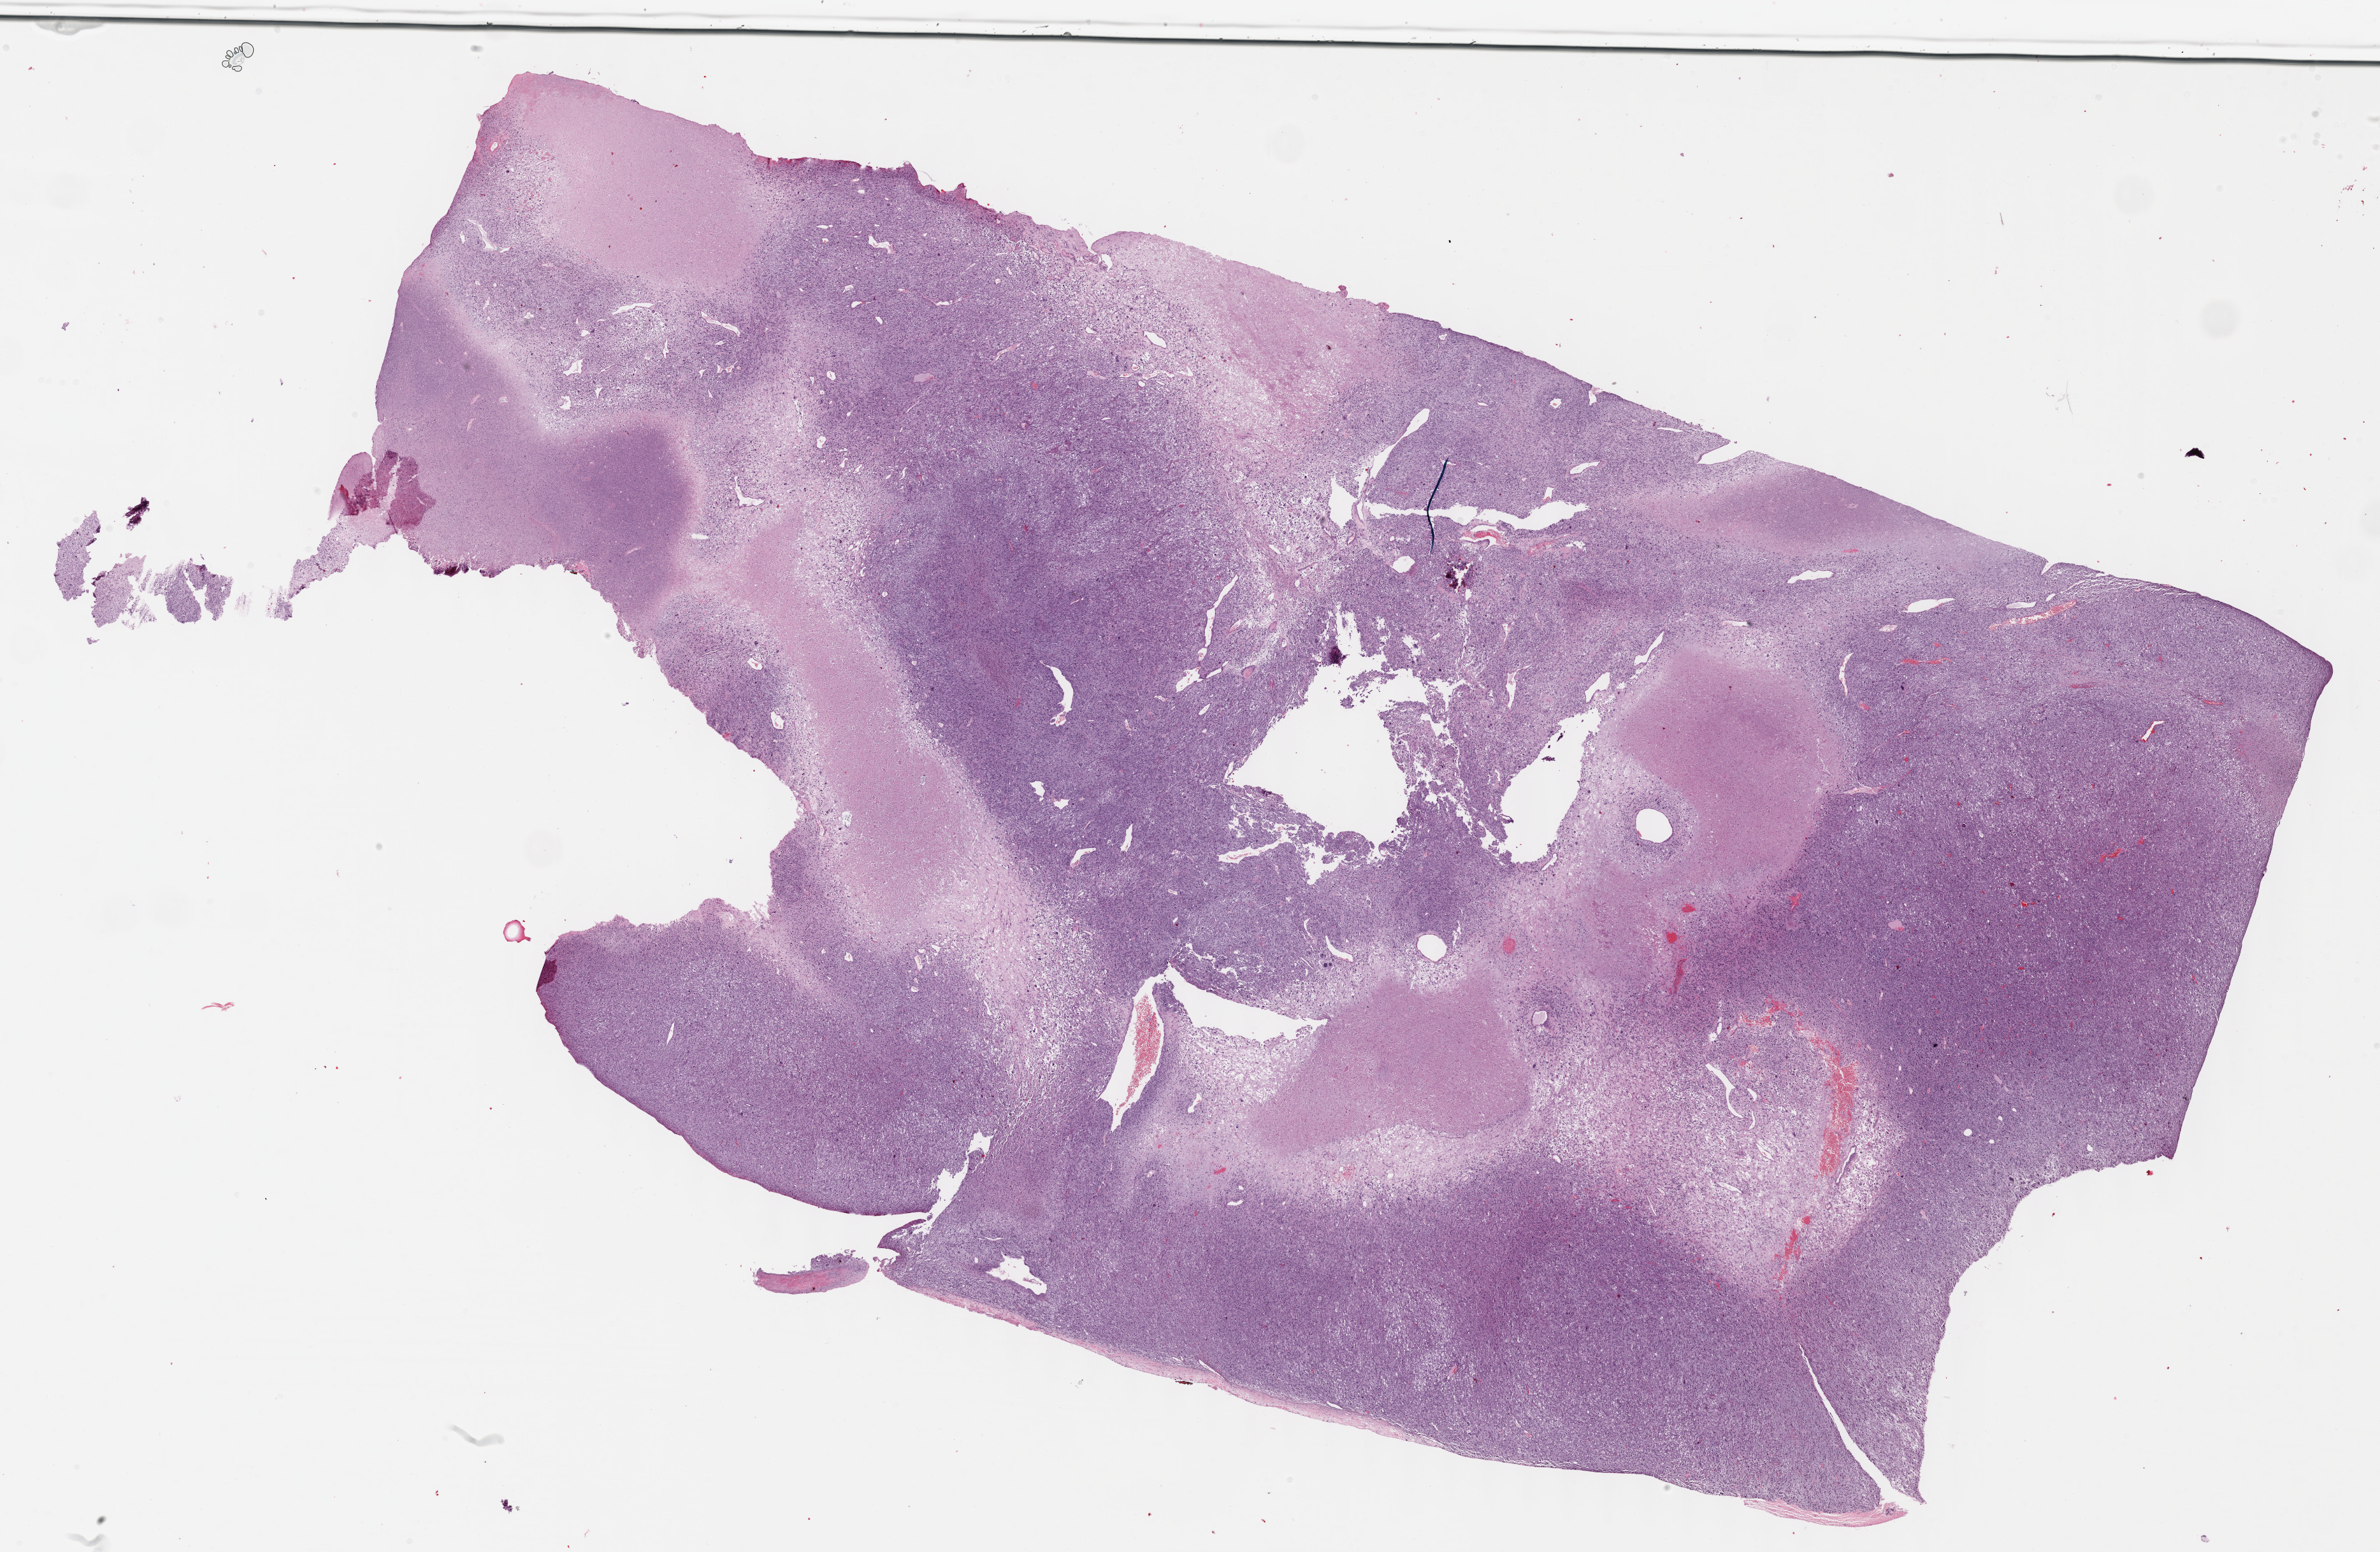
H&E whole-slide image, a low-resolution overview of the entire scanned area, about 30.2 x 19.7 mm (slide scanned at 40x). Formalin-fixed paraffin-embedded (FFPE) diagnostic section. Connective, subcutaneous and other soft tissues, primary tumour sample. Male patient; age at initial diagnosis 60 years.
Histologic diagnosis: Undifferentiated sarcoma (connective, subcutaneous and other soft tissues of lower limb and hip).